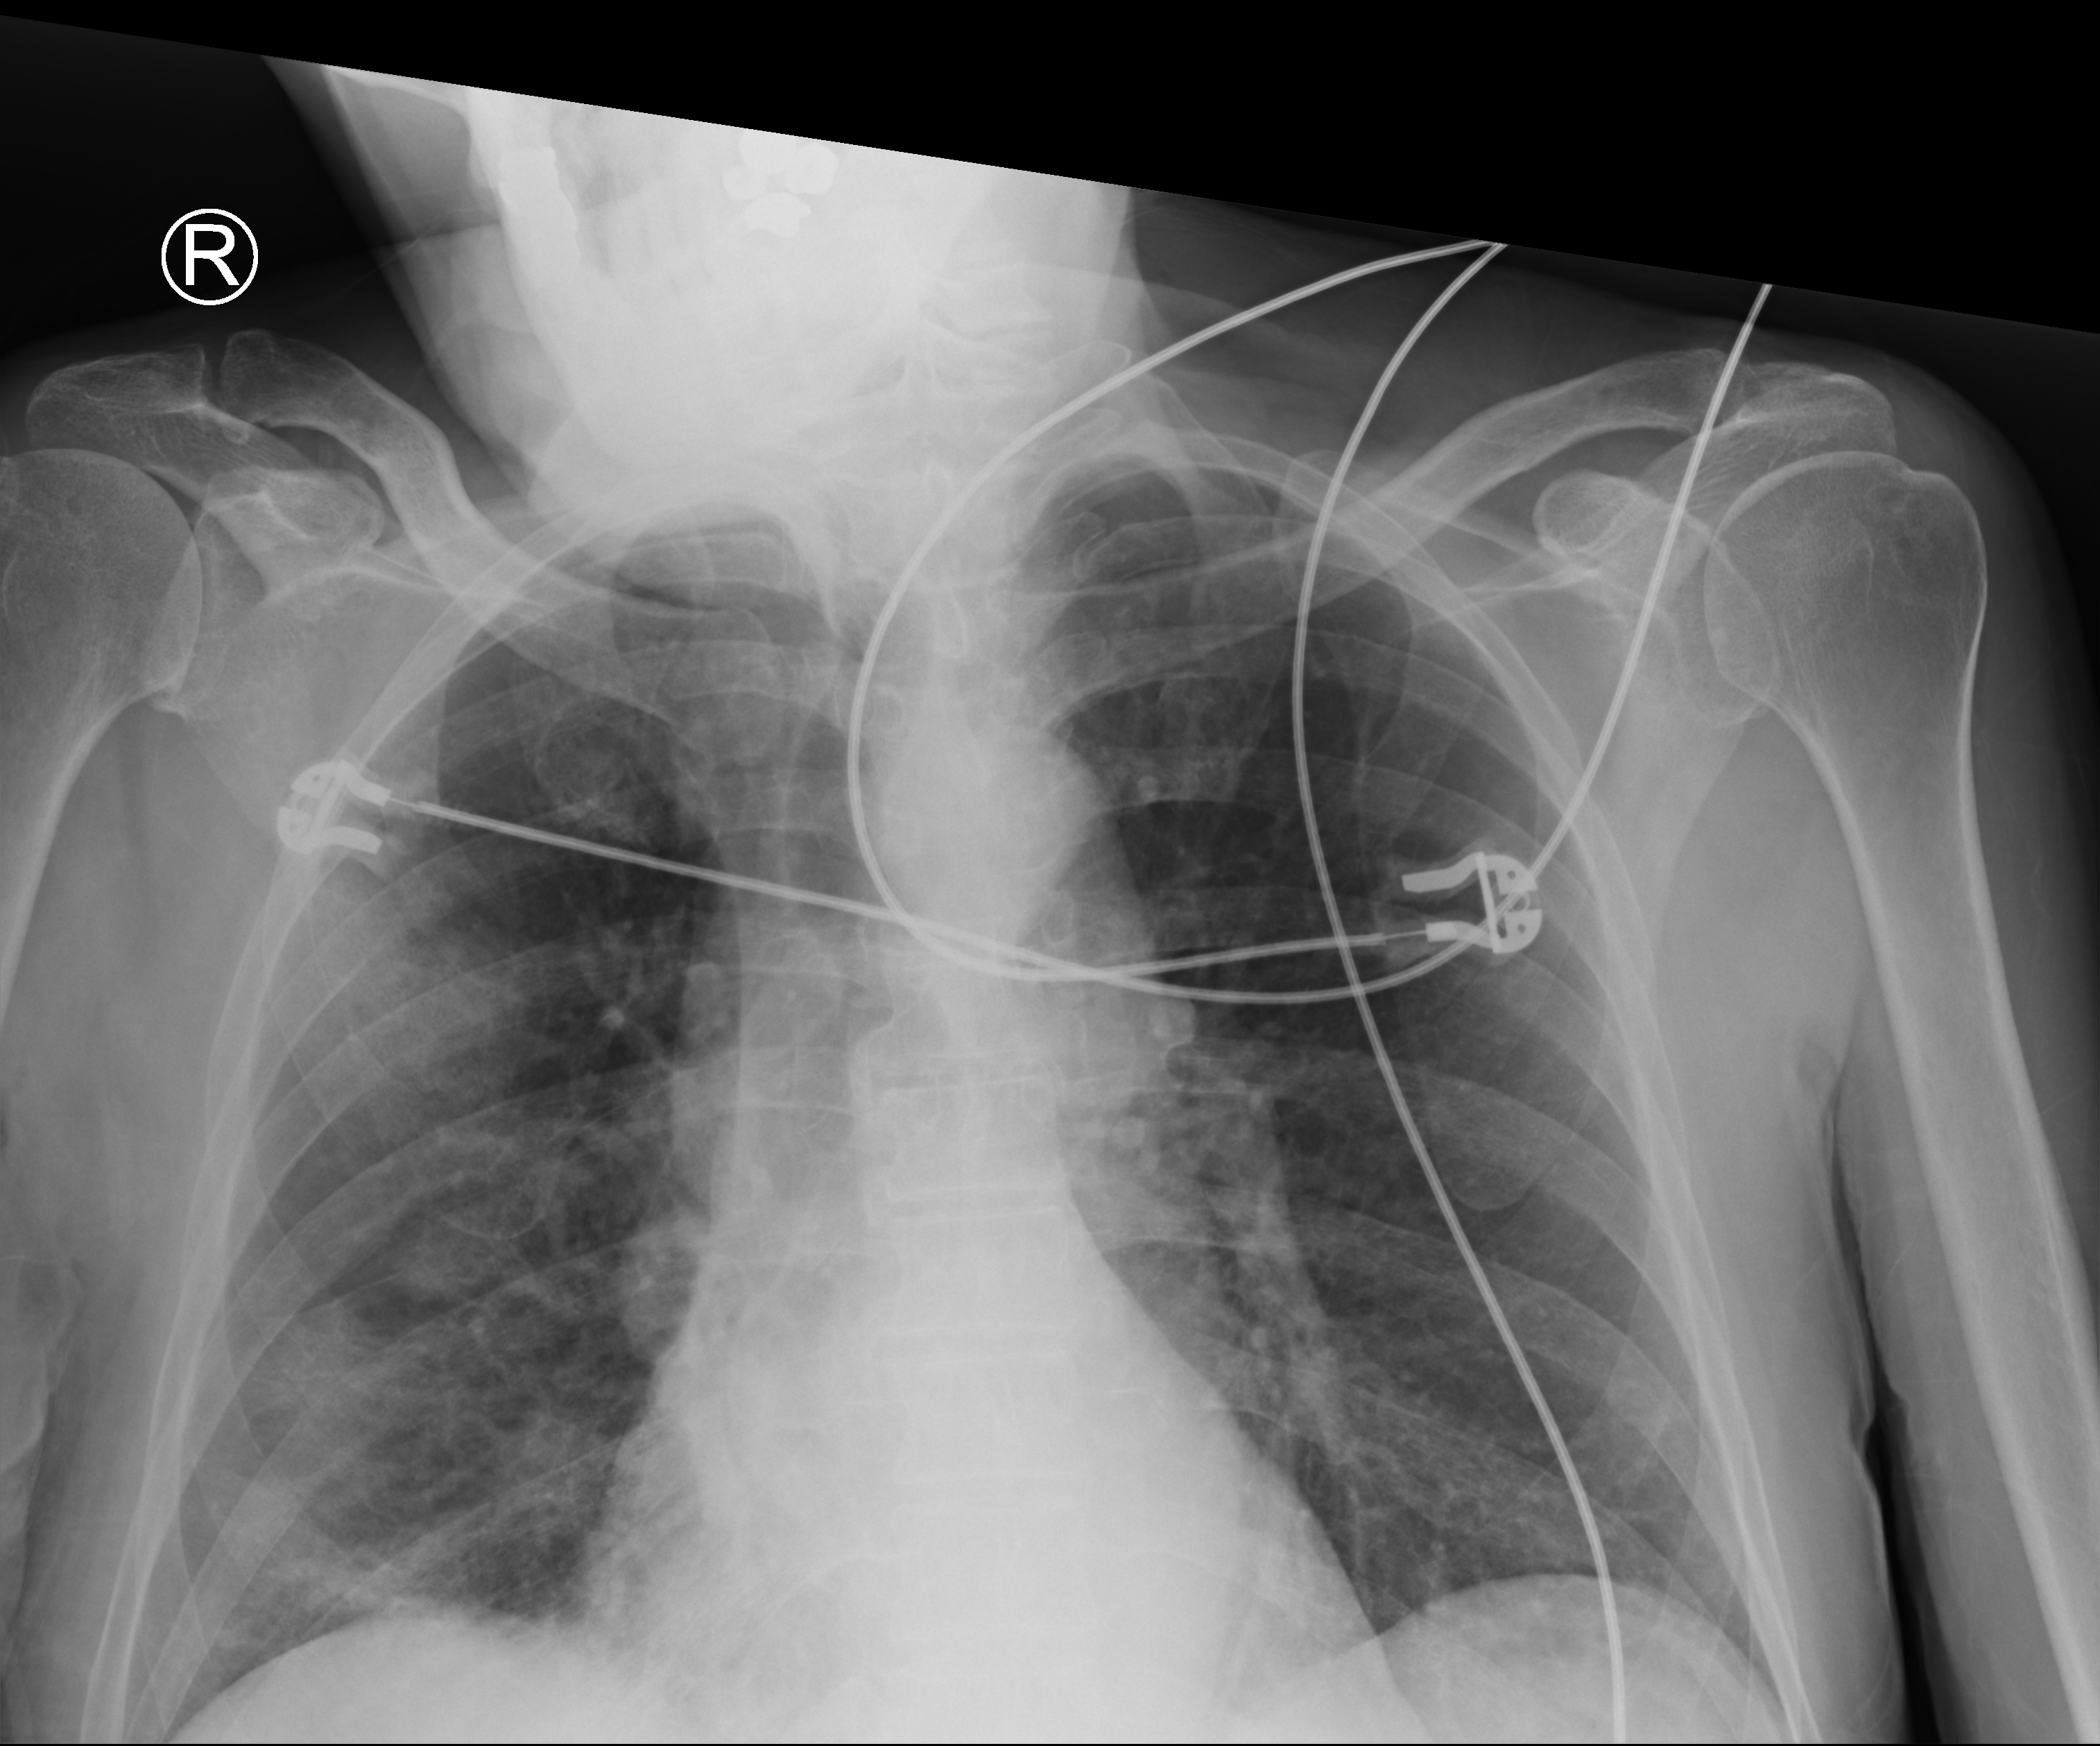
Chest X-ray (portable). Male patient hospitalised with COVID-19, age 60–74 years.
Hospital-stay facts (about this admission, not read from this image; timing relative to this image not recorded): hypertension (admission record): no; admitted to intensive care during this hospital stay: no.